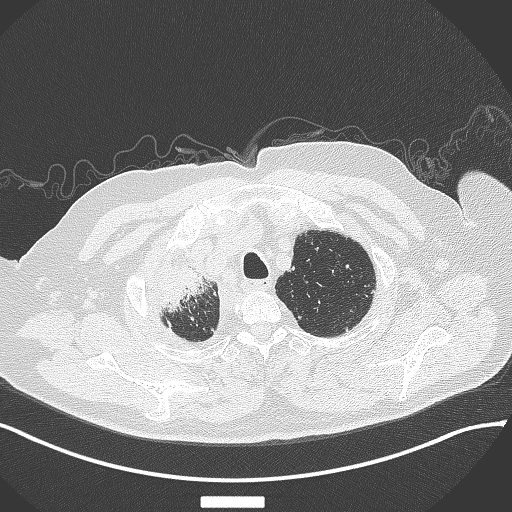
Chest CT, one axial slice; position 323 of 384 along the scan axis; reconstruction kernel B70f; lung window (W 1500 / L -600 HU); 1 mm slice thickness; 512 × 512 image matrix, field of view 400 × 400 mm. Patient: male, 69 years. Case-level facts recorded for this patient, not image findings: clinical TNM (as recorded): T4 N3 M1.
Annotated regions visible in this slice (rectangle marked by the reading radiologist):
- lung tumour (recorded histology: adenocarcinoma): bounding box (x1, y1, x2, y2) in pixels: (149, 257, 213, 311)